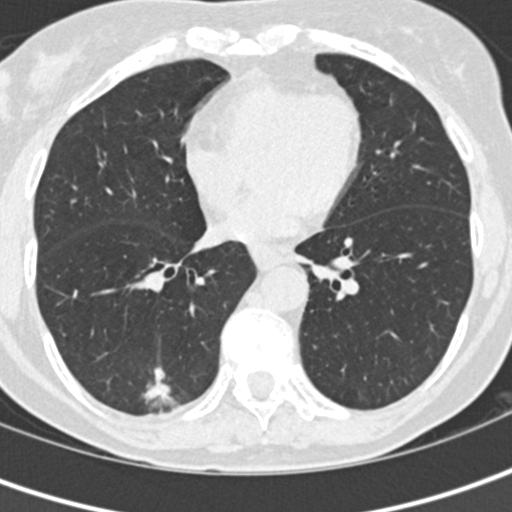
Low-dose screening chest CT, one axial slice. Slice 63 of 152 in the series (ordered by position). Reconstruction kernel B30f. Lung window (W 1500 / L -600 HU). 512 × 512 image matrix, field of view 280 × 280 mm.
Structures marked on this image (expert manual segmentation):
- lesion 1 (tumor, lower lobe of right lung): bounding box <143,367,177,407> (left, top, right, bottom; pixels)